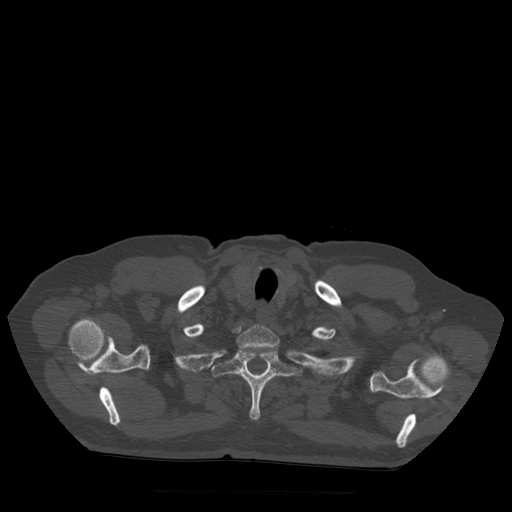
CT including the spine, one axial slice; position 429 of 522 along the scan axis; bone window (W 1800 / L 400 HU); 1.25 mm slice thickness; 512 × 512 image matrix, field of view 420 × 420 mm. Patient age 72 years. Case-level facts recorded for this patient, not image findings: primary cancer: prostate.
Outlined on this slice (semi-automatic segmentation, software-assisted and operator-edited):
- T1 vertebra: bounding box [x1, y1, x2, y2] px = [237, 326, 280, 352]
- T2 vertebra: [212, 349, 301, 420]